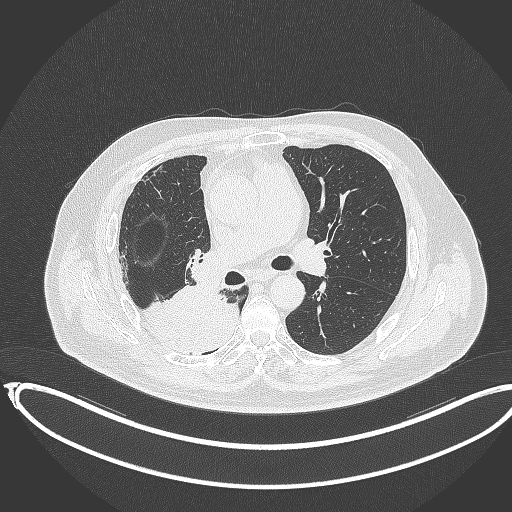
Chest CT, one axial slice; slice 206 of 403 in the series (ordered by position); 120 kVp; lung window (W 1500 / L -600 HU); 1 mm slice thickness; 512 × 512 image matrix, field of view 436 × 436 mm. Male patient, age 68 years. From the clinical record (not read from this slice): clinical TNM (as recorded): T2a N0 M0.
Outlined on this slice (rectangle marked by the reading radiologist):
- lung tumour (recorded histology: adenocarcinoma): bounding box (x1, y1, x2, y2) in pixels: (144, 287, 248, 365)